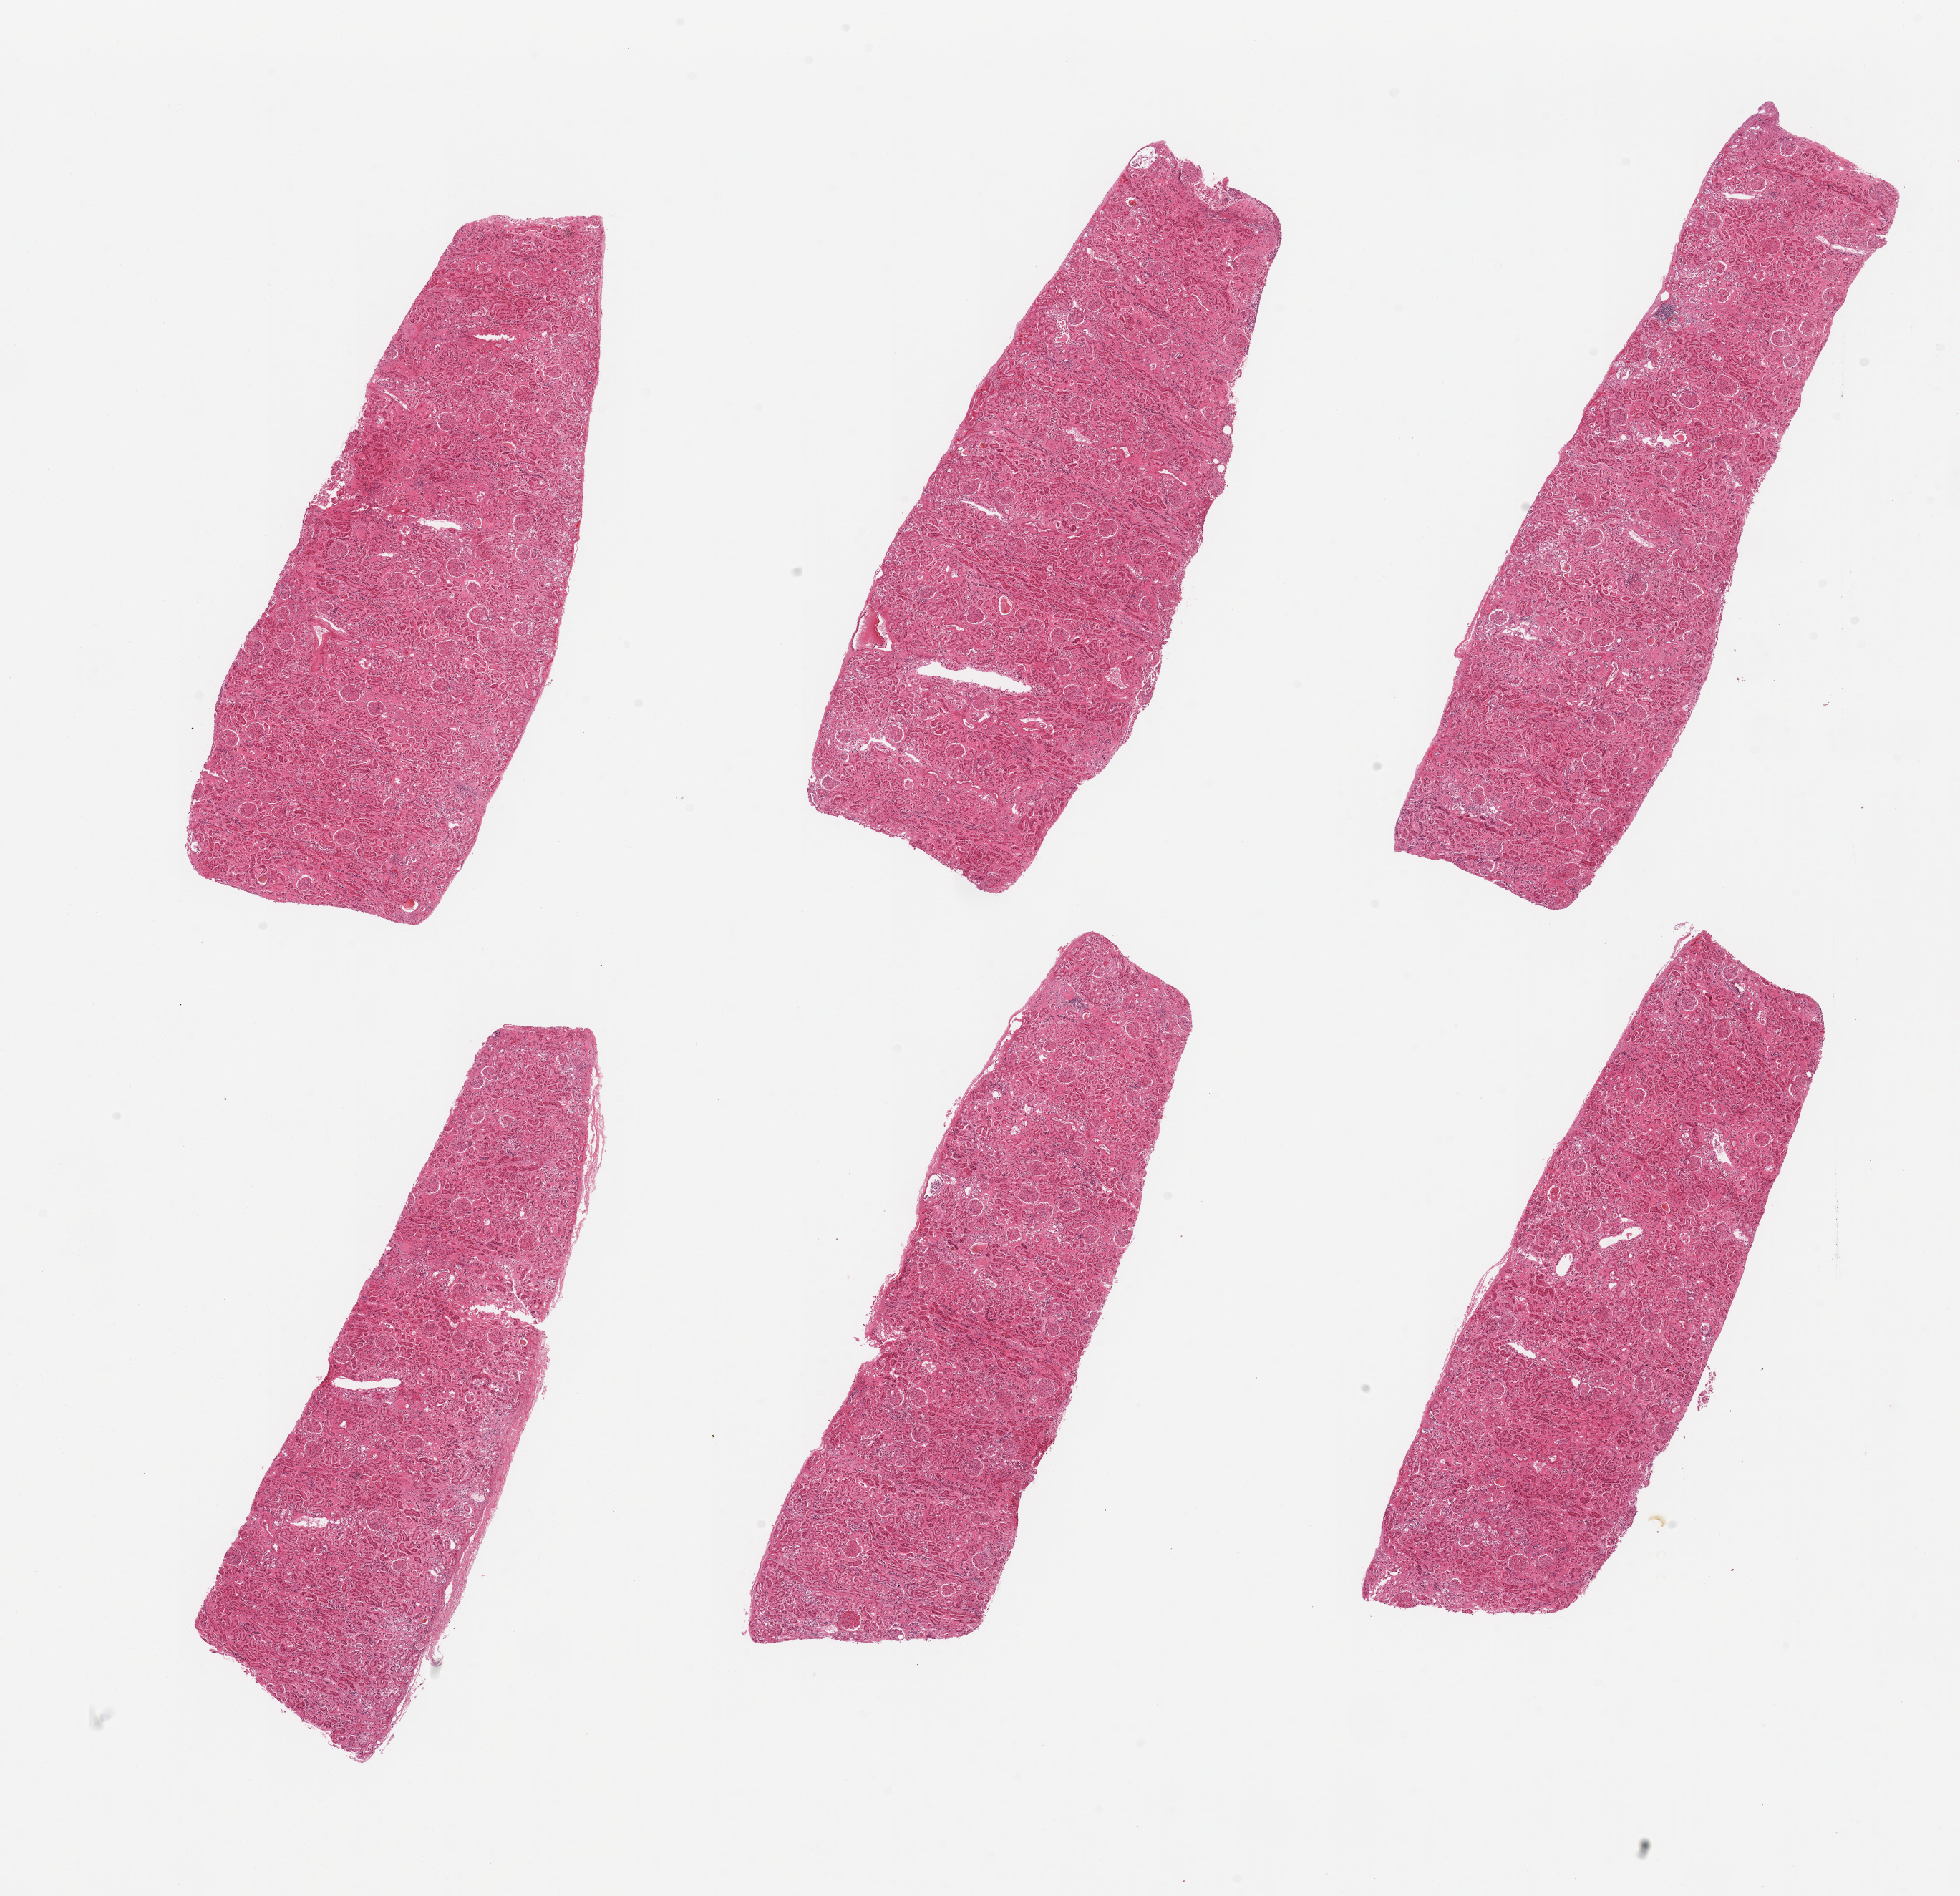
Digitized hematoxylin and eosin (H&E)-stained section — whole scanned area (about 21.7 x 21.0 mm, slide scanned at 20x) shown as a low-resolution overview, PAXgene-fixed paraffin-embedded (PFPE) section, target tissue: renal cortex, donor tissue sample. Donor sex: male.
Review note (as recorded): 6 pieces, glomeruli present, tubules with advanced autolysis.